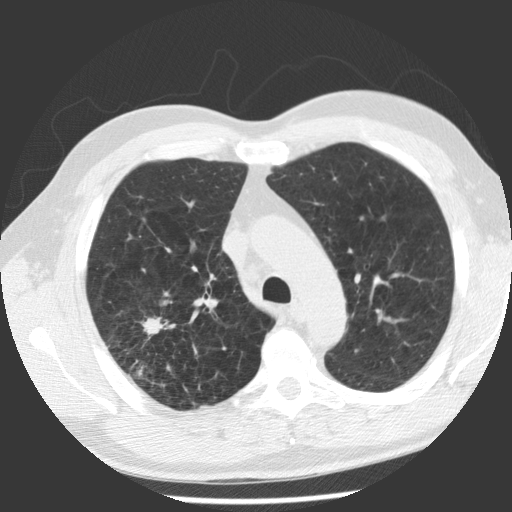
Low-dose screening chest CT, one axial slice; position 82 of 112 along the scan axis; reconstruction kernel STANDARD; 140 kVp; lung window (W 1500 / L -600 HU); 512 × 512 image matrix, field of view 344 × 344 mm.
Annotated regions visible in this slice (expert manual segmentation):
- lesion 1 (tumor, upper lobe of right lung): bounding box (x1, y1, x2, y2) in pixels: (141, 317, 164, 336)